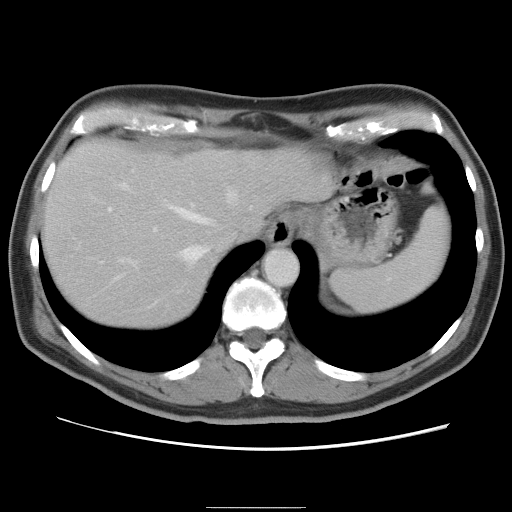
Contrast-enhanced abdominal CT, one axial slice; slice 67 of 87 in the series (ordered by position); 120 kVp; soft-tissue window (W 400 / L 40 HU); 5 mm slice thickness; 512 × 512 image matrix. Male patient, age 63 years. From the clinical record (not read from this slice): diagnosis: colorectal cancer liver metastases, imaged before liver resection; multiple liver metastases: no; largest metastasis: 9 cm.
Outlined on this slice (expert manual segmentation):
- hepatic veins: box from (x=100, y=182) to (x=238, y=266) px
- liver: (x=42, y=141)–(x=329, y=329)
- planned liver remnant (the part of the liver to remain after resection): (x=42, y=164)–(x=216, y=329)
- portal vein (with intrahepatic branches): (x=107, y=206)–(x=158, y=283)